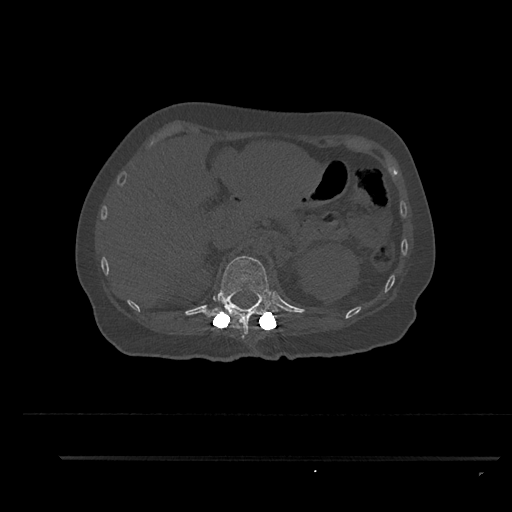
CT including the spine, one axial slice; slice 259 of 797 in the series (ordered by position); 120 kVp; bone window (W 1800 / L 400 HU); 0.5 mm slice thickness; 512 × 512 image matrix, field of view 408 × 408 mm. Female patient, age 44 years. Case-level facts recorded for this patient, not image findings: primary cancer: renal.
Structures marked on this image (semi-automatic segmentation, software-assisted and operator-edited):
- T12 vertebra: bounding box <204,256,279,339> (left, top, right, bottom; pixels)